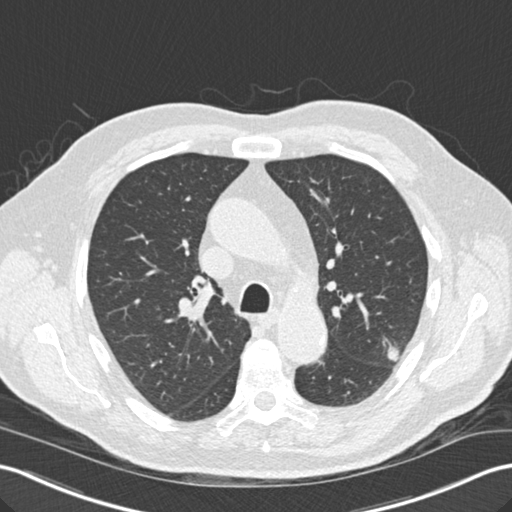
Low-dose screening chest CT, one axial slice; slice 102 of 157 in the series (ordered by position); 120 kVp; lung window (W 1500 / L -600 HU); 2 mm slice thickness; 512 × 512 image matrix, field of view 354 × 354 mm.
Annotated regions visible in this slice (outlined manually by an expert reader):
- lesion 1 (tumor, upper lobe of left lung): bounding box (x1, y1, x2, y2) in pixels: (383, 339, 399, 361)